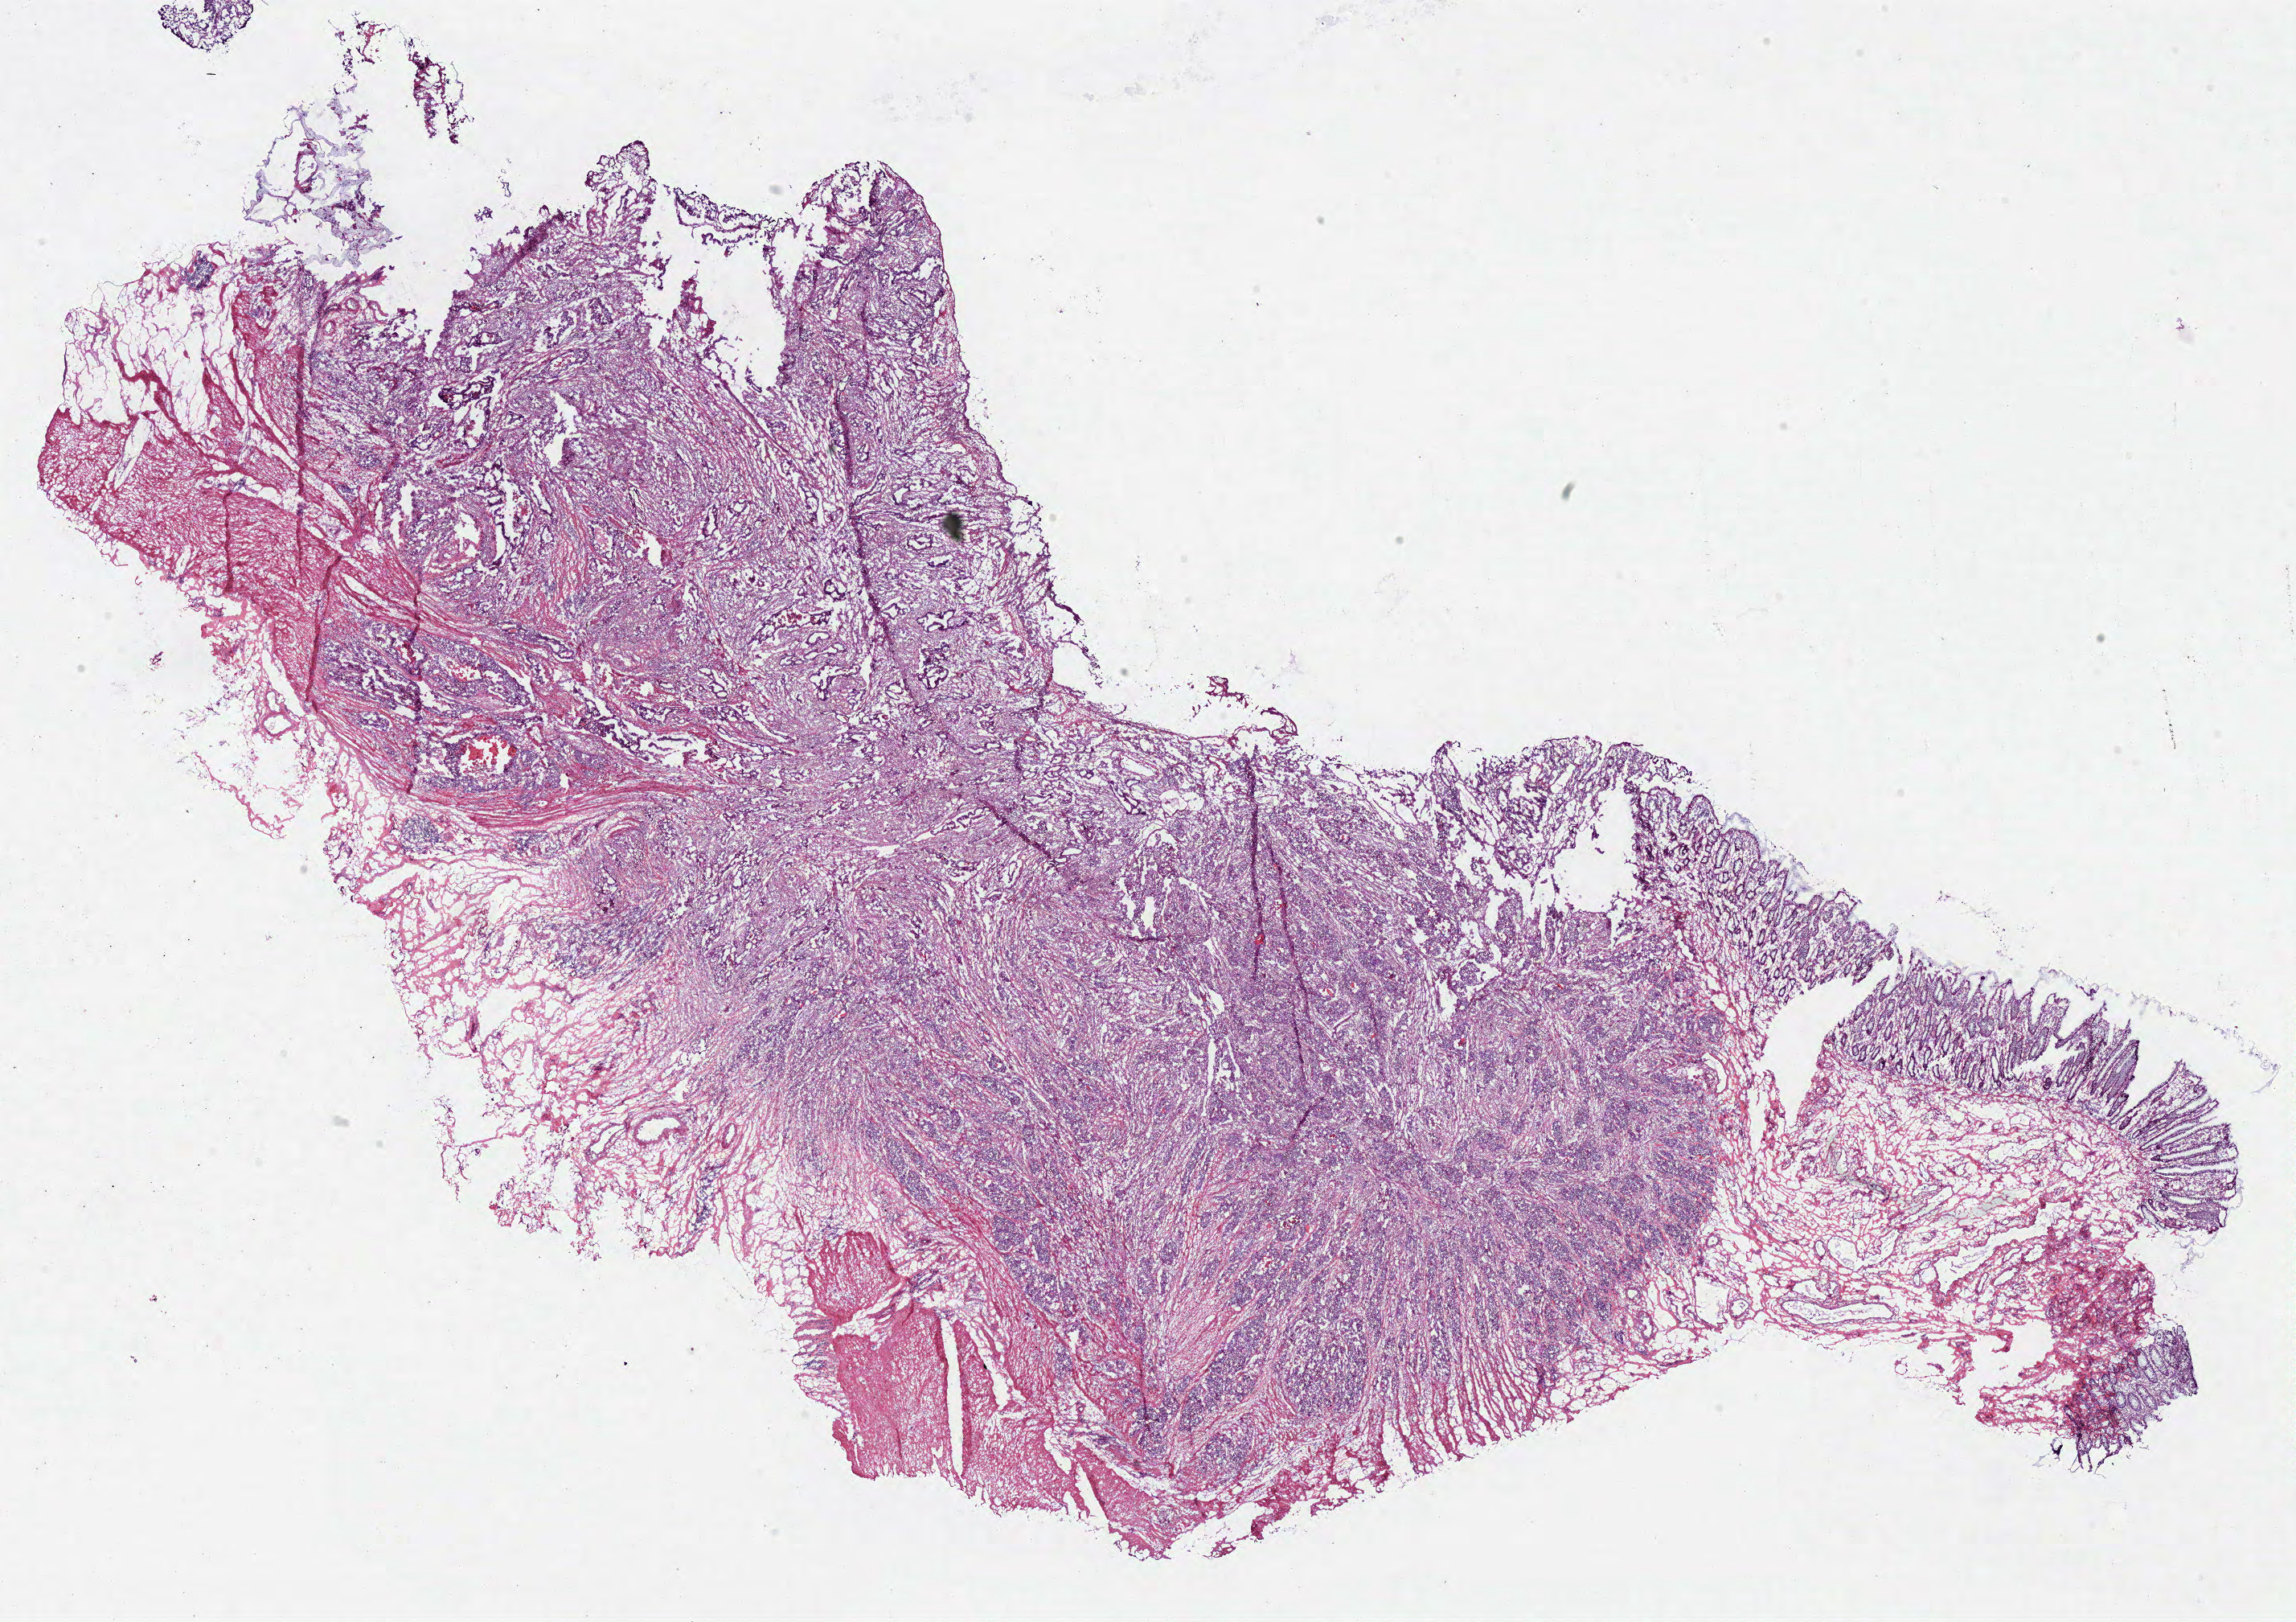
Whole-slide histology image, H&E, whole scanned area (about 22.5 x 15.9 mm) shown as a low-resolution overview. Frozen section from the bottom of the tissue portion. Primary tumour sample from the rectum. Patient: male, age at initial diagnosis 71 years. Composition of this section per pathologist review: tumour cells 78%, tumour nuclei 80%, normal cells 5%, stromal cells 15%, necrosis 2%.
- histologic diagnosis: Adenocarcinoma, NOS (rectosigmoid junction)
- AJCC pathologic stage: IVA (7th edition)